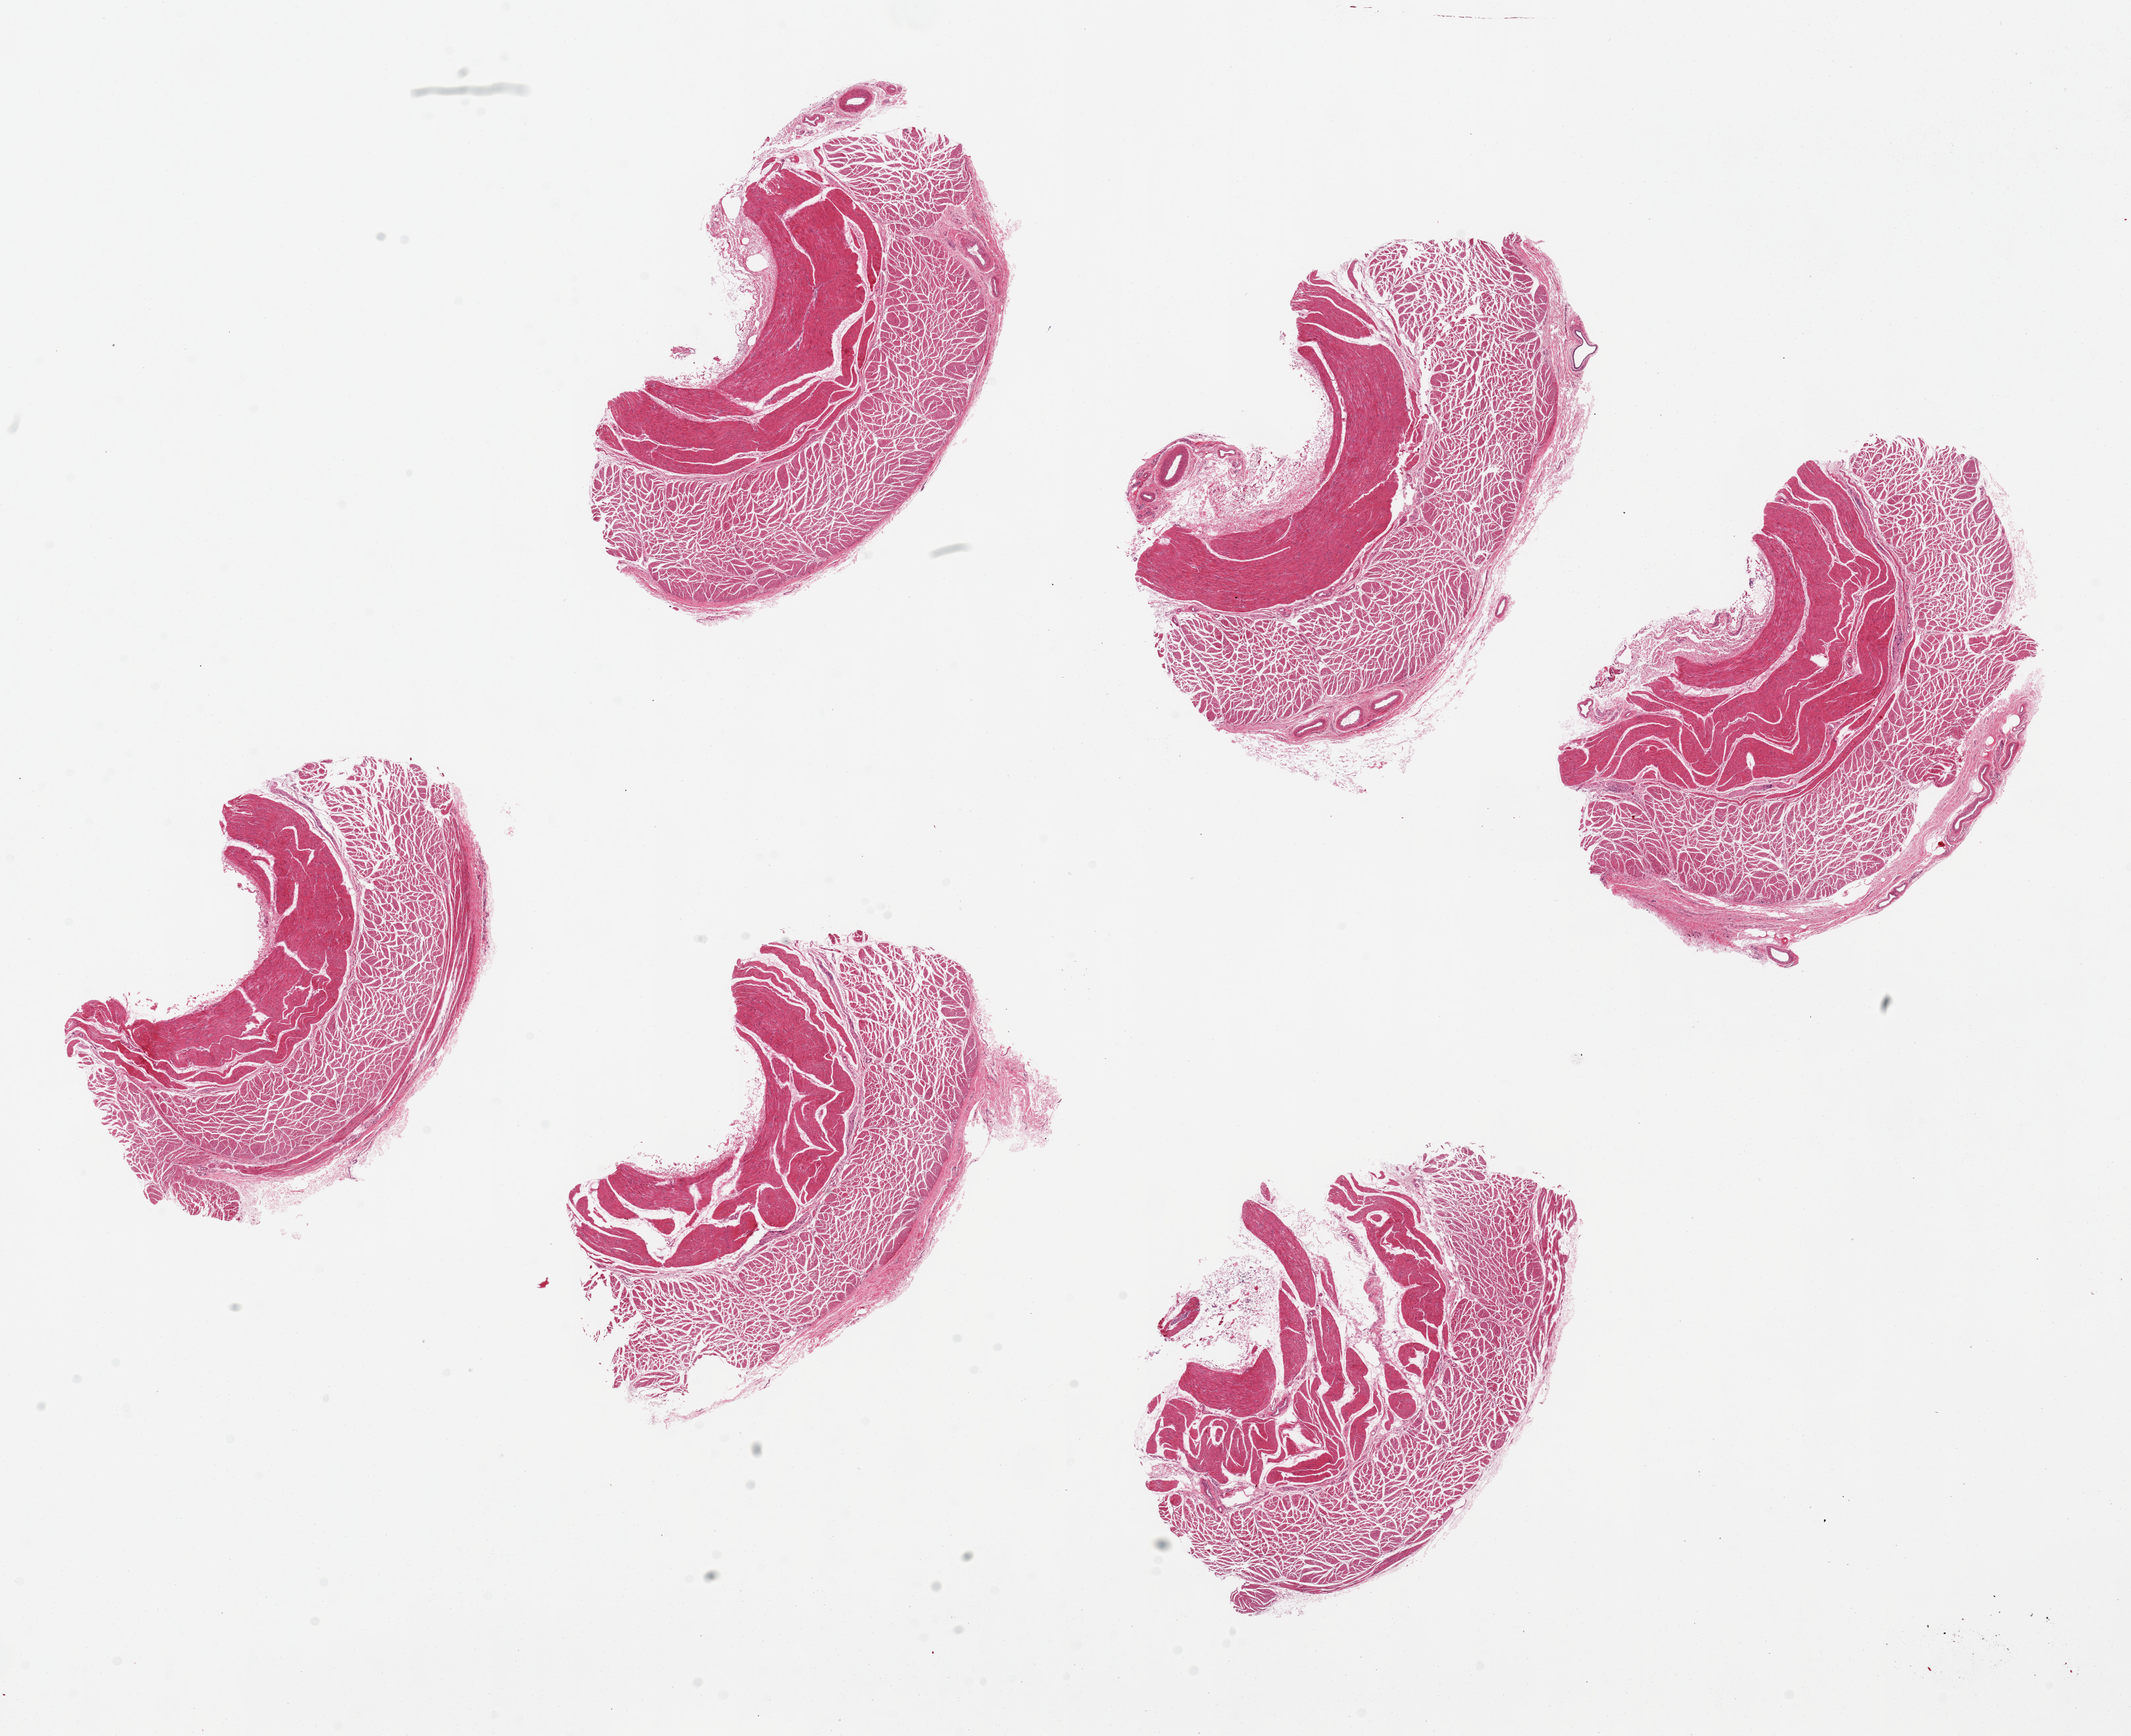
Hematoxylin and eosin (H&E) whole-slide image, brightfield — whole scanned area (about 25.6 x 20.8 mm, acquisition: 20x scan) shown as a low-resolution overview. PAXgene-fixed paraffin-embedded (PFPE) section. Sampled site (target tissue): esophageal muscle. Tissue donor sample. Donor sex: female.
Review note (as recorded): 6 pieces, up to 6x4mm. Well dissected.